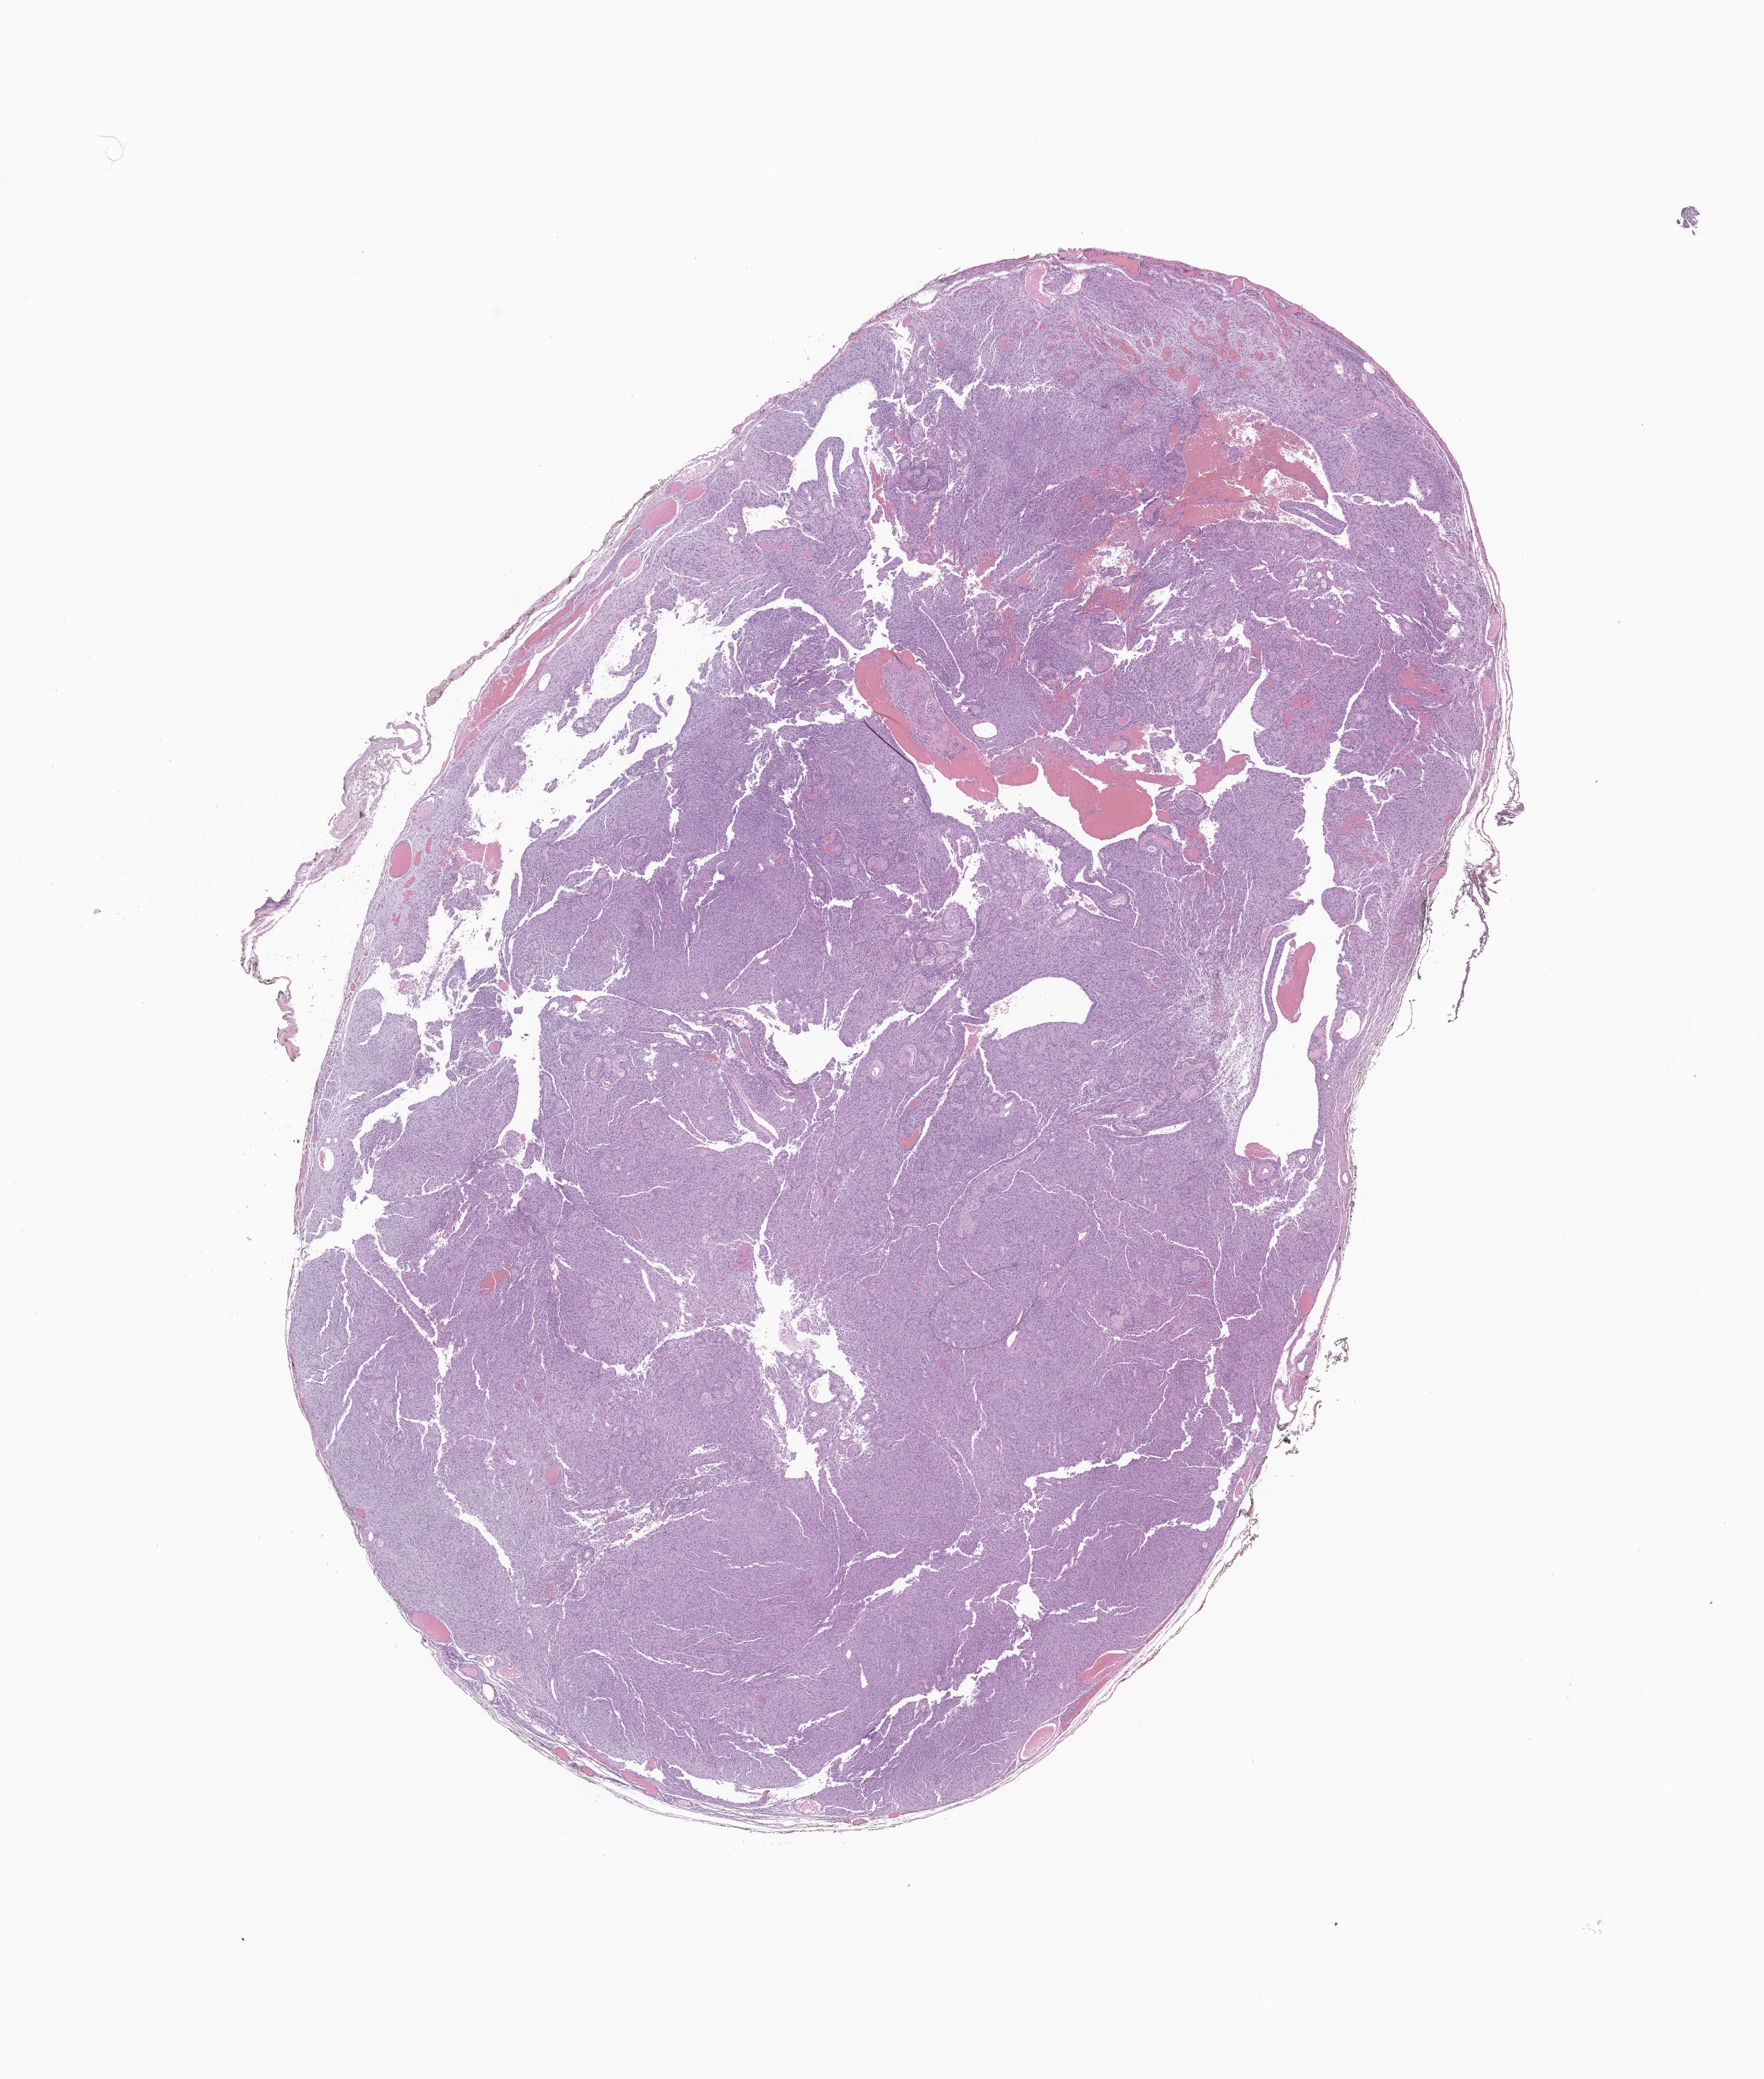
Digitized H&E-stained section of tumor tissue from the spinal cord, whole scanned area (about 13.5 x 15.9 mm) shown as a low-resolution overview; FFPE section. Patient: male, age 211 months (17 years 7 months).
Diagnosis: Neoplasm, uncertain whether benign or malignant.